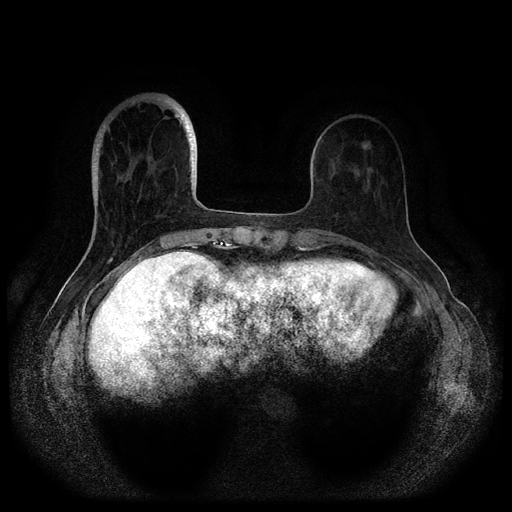
Breast MRI (dynamic contrast-enhanced, multi-phase), one axial slice; dynamic contrast-enhanced series, time point 2 of 5 at this slice position (early post-contrast); 1.5 T; TE 2.6 ms, TR 5.3 ms; 512 × 512 image matrix, field of view 350 × 350 mm. Female patient, age 82 years.
Structures marked on this image (semi-automatic segmentation, software-assisted and operator-edited):
- breast lesion (labelled benign in the annotation): box from (x=364, y=145) to (x=368, y=148) px